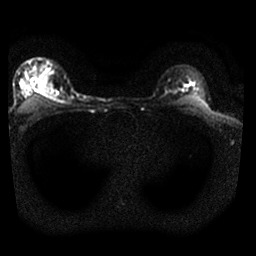
Breast MRI, one axial slice. Position 25 of 25 along the scan axis. Diffusion-weighted series; image 2 of 4 stored at this slice position (different b-values; order by instance number). 1.5 T. 256 × 256 image matrix, field of view 310 × 310 mm. Female patient.
Structures marked on this image (manually delineated by an expert):
- tumour on diffusion-weighted imaging: bounding box [x1, y1, x2, y2] px = [39, 78, 52, 94]